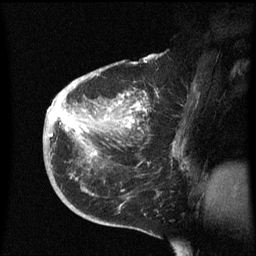
Breast MRI (dynamic contrast-enhanced), one sagittal slice; slice 33 of 60 in the series (ordered by position); dynamic contrast-enhanced series, image 2 of 3 at this slice position (ordered by acquisition); 1.5 T; TE 4.2 ms, TR 8.4 ms; 256 × 256 image matrix. Female patient, age 38 years. From the clinical record (not read from this slice): setting: breast cancer imaged before/during neoadjuvant chemotherapy; receptor status: HER2-positive.
Outlined on this slice (semi-automatically segmented with operator editing):
- analysis volume of interest (the breast-tissue region the enhancement analysis was run in; not a lesion): bounding box <43,78,187,213> (left, top, right, bottom; pixels)
- tumour enhancement mask (voxels above the 70 % enhancement threshold inside the analysis volume of interest): <51,98,145,155>